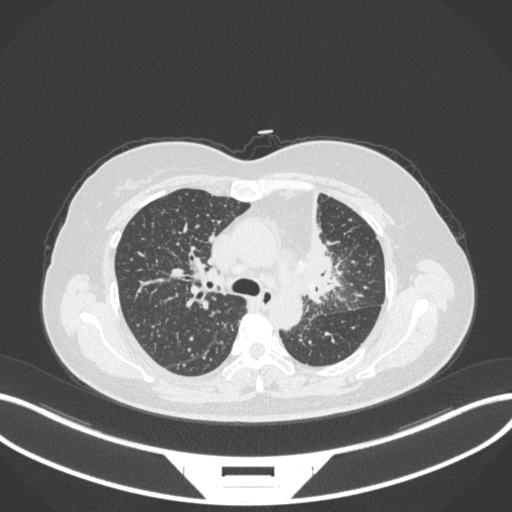
Chest CT, one axial slice; position 224 of 348 along the scan axis; lung window (W 1500 / L -600 HU); 1 mm slice thickness; 512 × 512 image matrix, field of view 400 × 400 mm. Female patient, age 49 years. Case-level facts recorded for this patient, not image findings: clinical TNM (as recorded): T1c N0 M1.
Annotated regions visible in this slice (rectangle marked by the reading radiologist):
- lung tumour (recorded histology: adenocarcinoma): bounding box <291,186,349,307> (left, top, right, bottom; pixels)